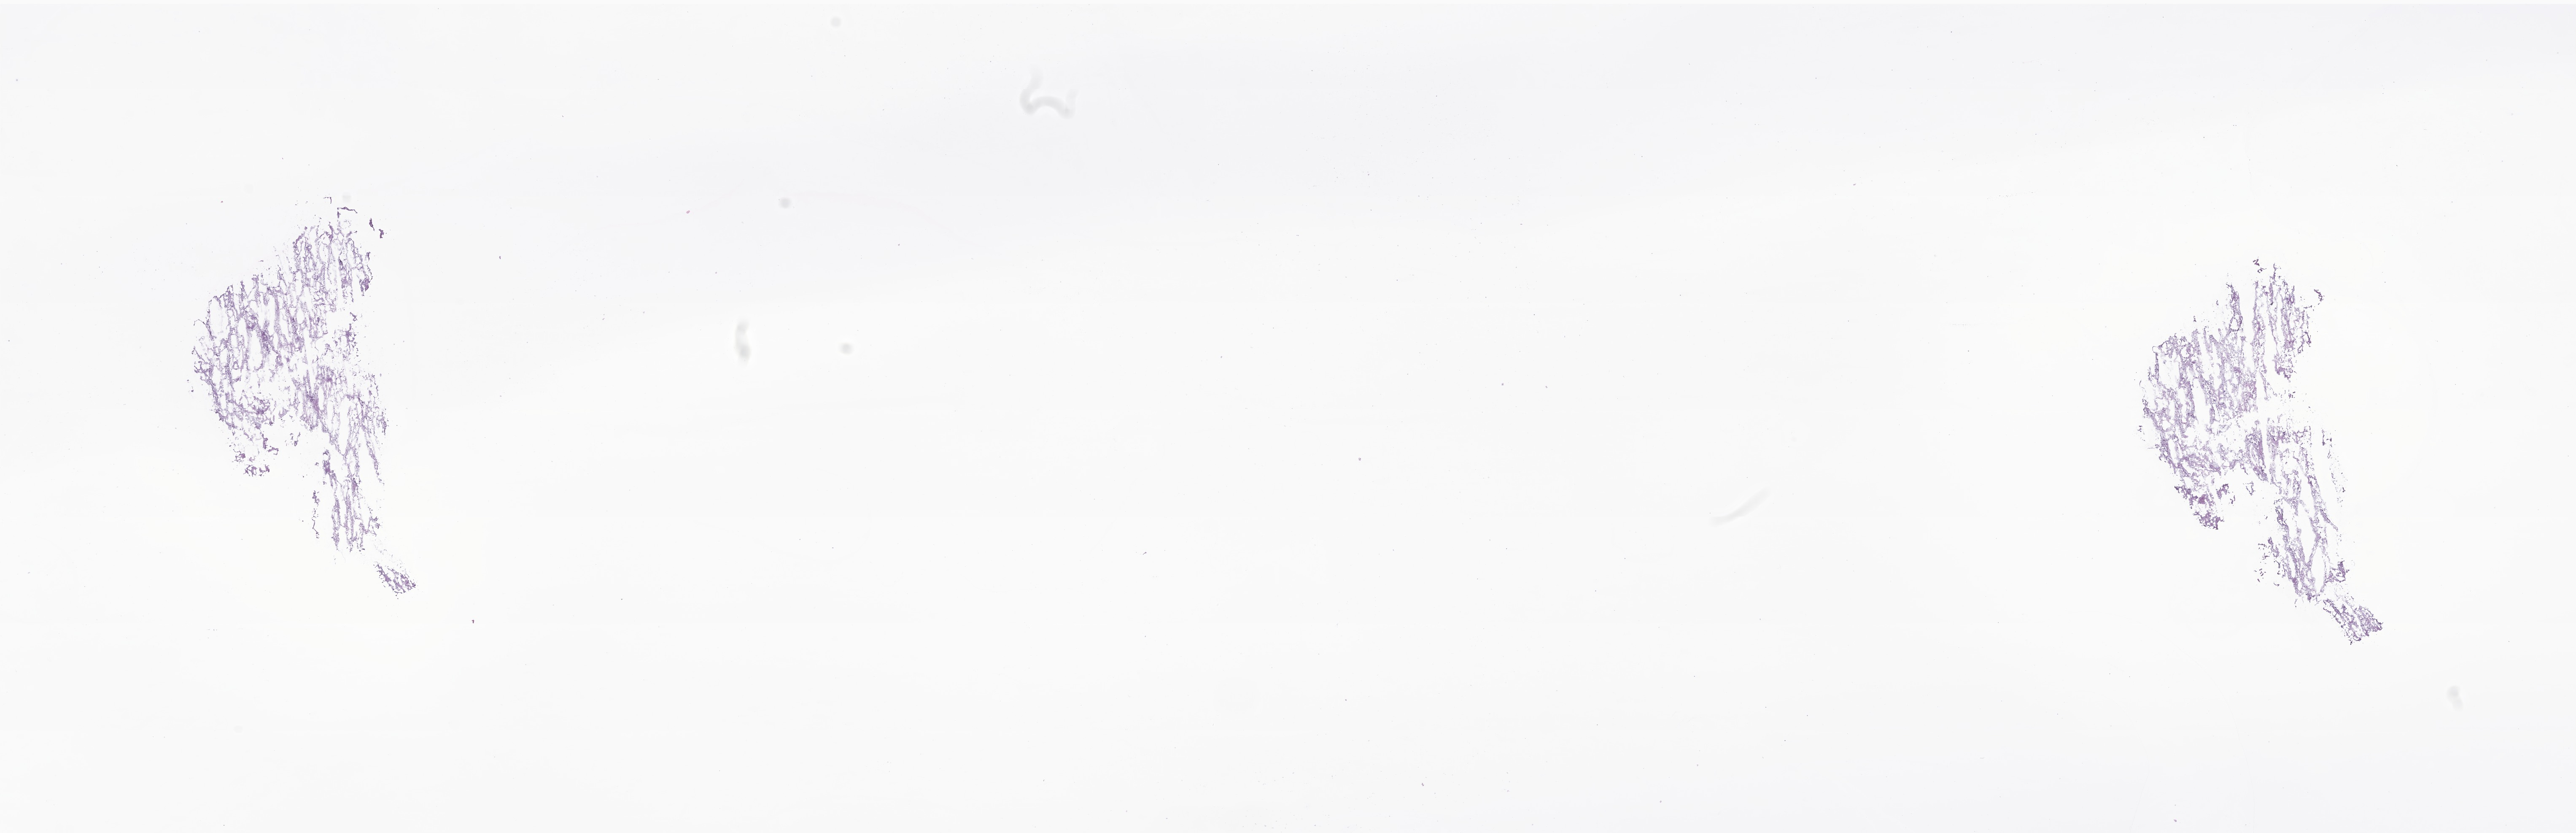
Haematoxylin and eosin whole-slide image of tumor tissue from the cerebellum — low-resolution overview of the scanned area, about 25.8 x 8.3 mm; cryosection (OCT / tissue freezing medium). Female patient, age 144 months (12 years).
Diagnosis (ICD-O-3 morphology term): Pilocytic astrocytoma.